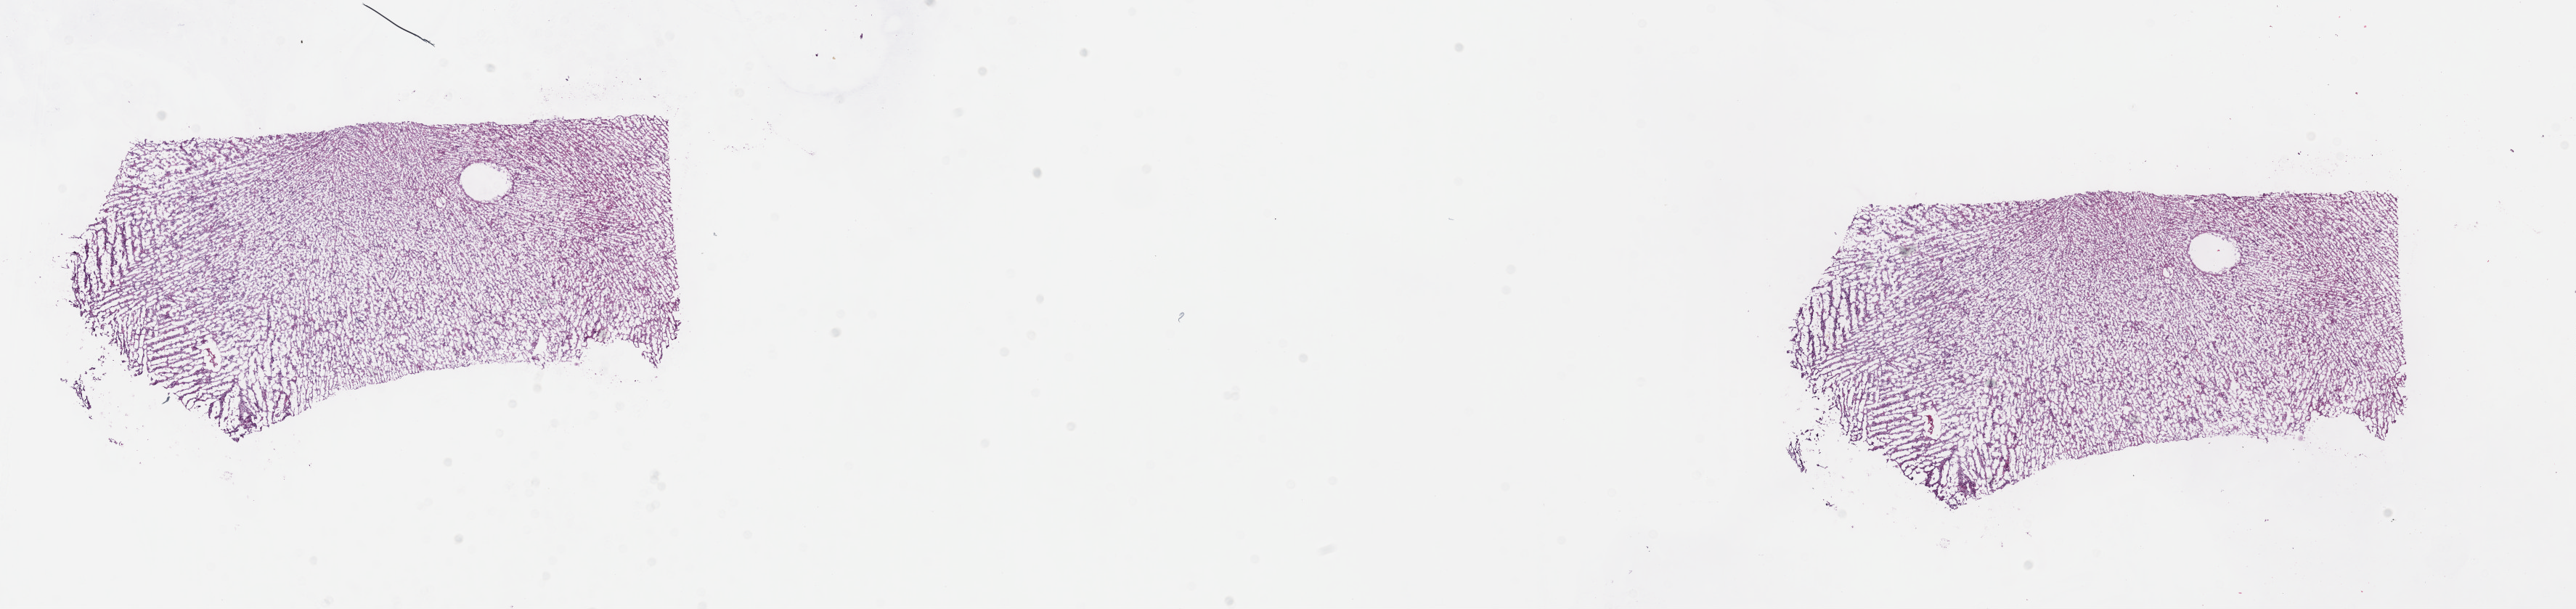
H&E-stained whole-slide image, low-resolution overview of the scanned area, about 28.7 x 6.8 mm (from a 40x scan). Frozen section. Sample: primary tumour, brain. Male patient; age at initial diagnosis 60 years. Histologic grade: G2 (moderately differentiated). Slide review estimates, as recorded: tumour cells 30%, tumour nuclei 70%, normal cells 10%, stromal cells 60%, necrosis 0%. Inflammatory infiltration, as recorded: lymphocyte infiltration 0%, monocyte infiltration 0%, neutrophil infiltration 0%.
Pathologic diagnosis: Mixed glioma (cerebrum). Laterality: right.